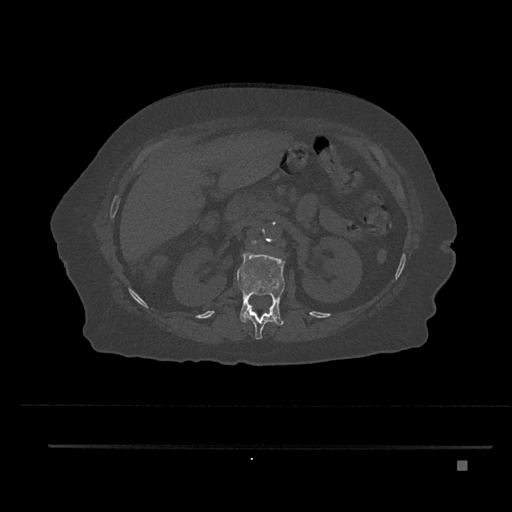
CT including the spine, one axial slice. Slice 234 of 797 in the series (ordered by position). Bone window (W 1800 / L 400 HU). 0.5 mm slice thickness. 512 × 512 image matrix, field of view 437 × 437 mm. Patient: female, 76 years. Case-level facts recorded for this patient, not image findings: primary cancer: lung; vertebrae with lytic lesions (as recorded): T11, L3.
Annotated regions visible in this slice (semi-automatic segmentation, software-assisted and operator-edited):
- L1 vertebra: bounding box [x1, y1, x2, y2] px = [237, 250, 285, 325]
- L2 vertebra: [251, 240, 257, 247]
- T12 vertebra: [244, 305, 276, 340]